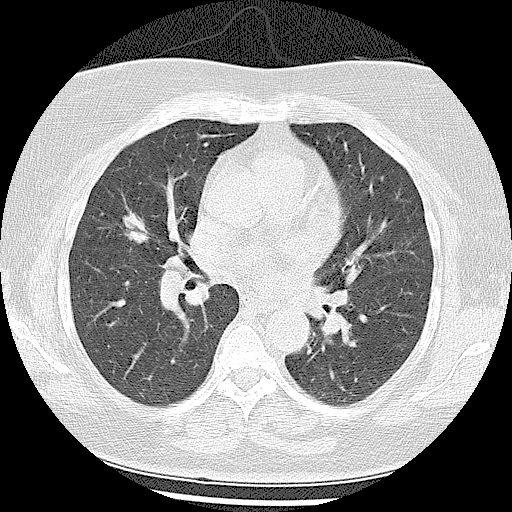
Low-dose screening chest CT, one axial slice; slice 53 of 102 in the series (ordered by position); reconstruction kernel LUNG; lung window (W 1500 / L -600 HU); 2.5 mm slice thickness; 512 × 512 image matrix.
Outlined on this slice (outlined manually by an expert reader):
- lesion 1 (tumor, middle lobe of right lung): bounding box (x1, y1, x2, y2) in pixels: (122, 209, 151, 244)